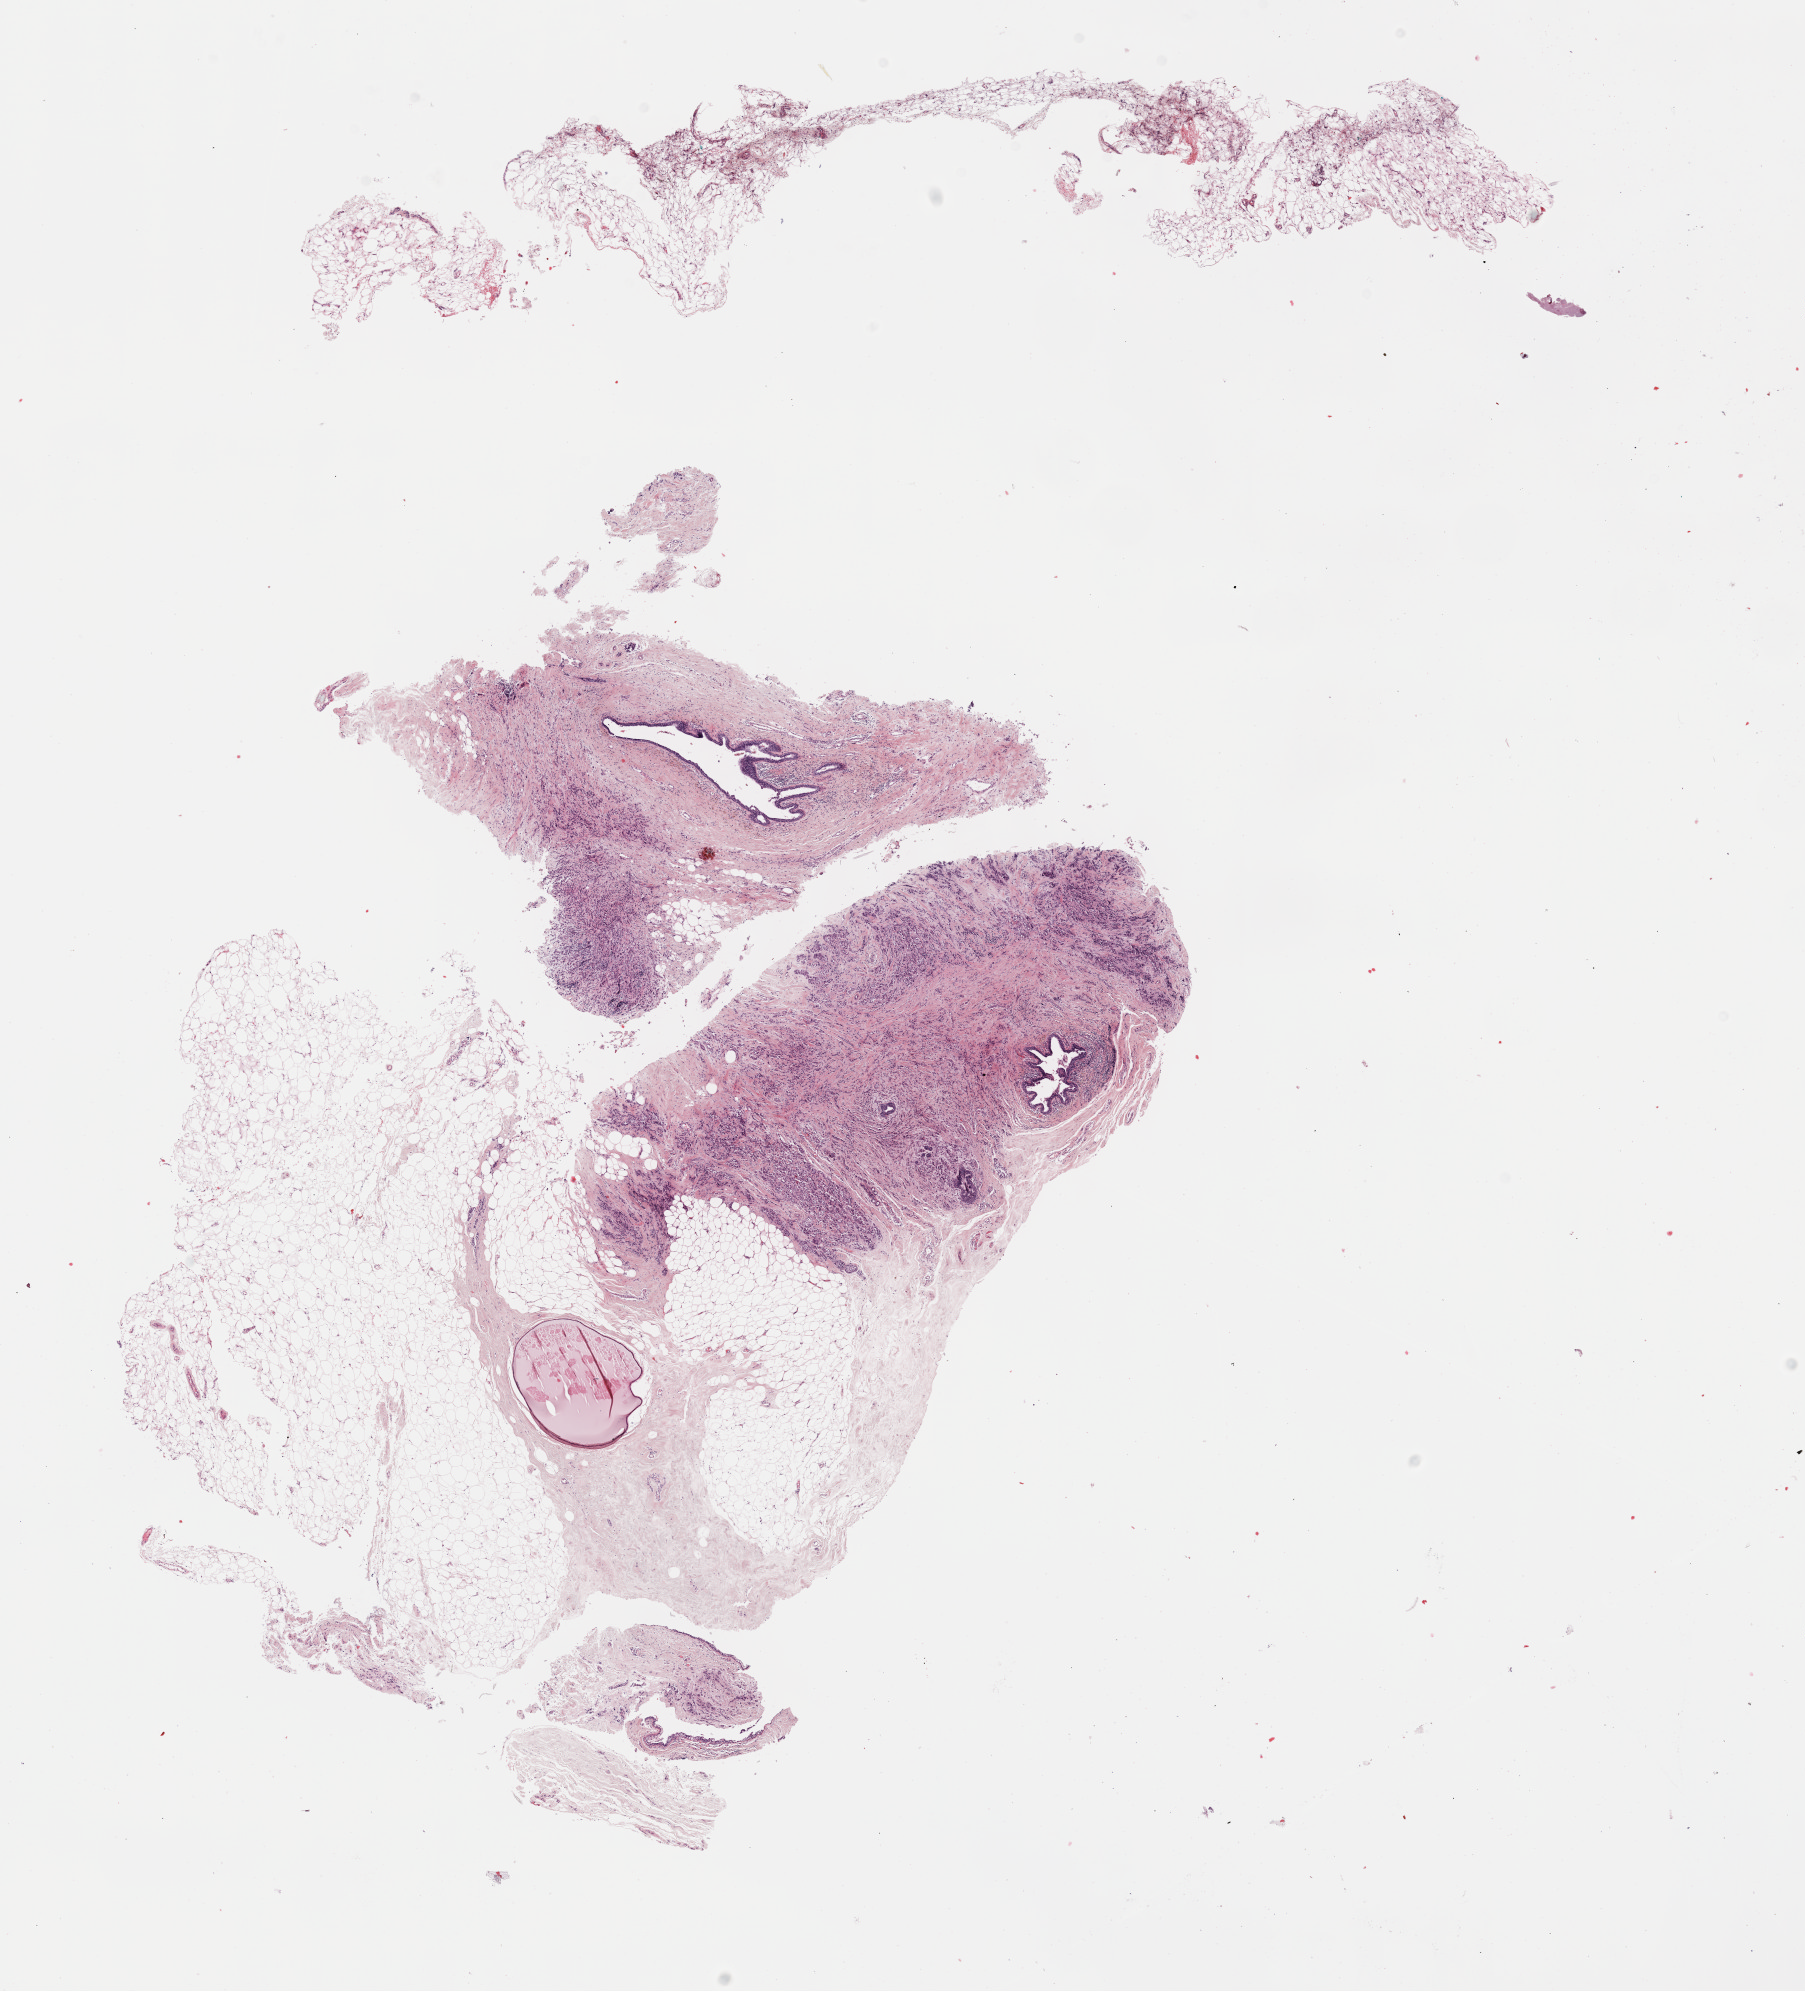
Whole-slide histology image, H&E — whole scanned area (about 14.6 x 16.1 mm) shown as a low-resolution overview. Formalin-fixed paraffin-embedded (FFPE) diagnostic section. Sample: primary tumour, breast. Patient: female, age at initial diagnosis 56 years.
AJCC pathologic stage: IIIC. Laterality: left. Pathologic diagnosis: Lobular carcinoma, NOS. Lymph nodes positive (case pathology): 19 of 22 examined. TNM: T3 N3a M0.